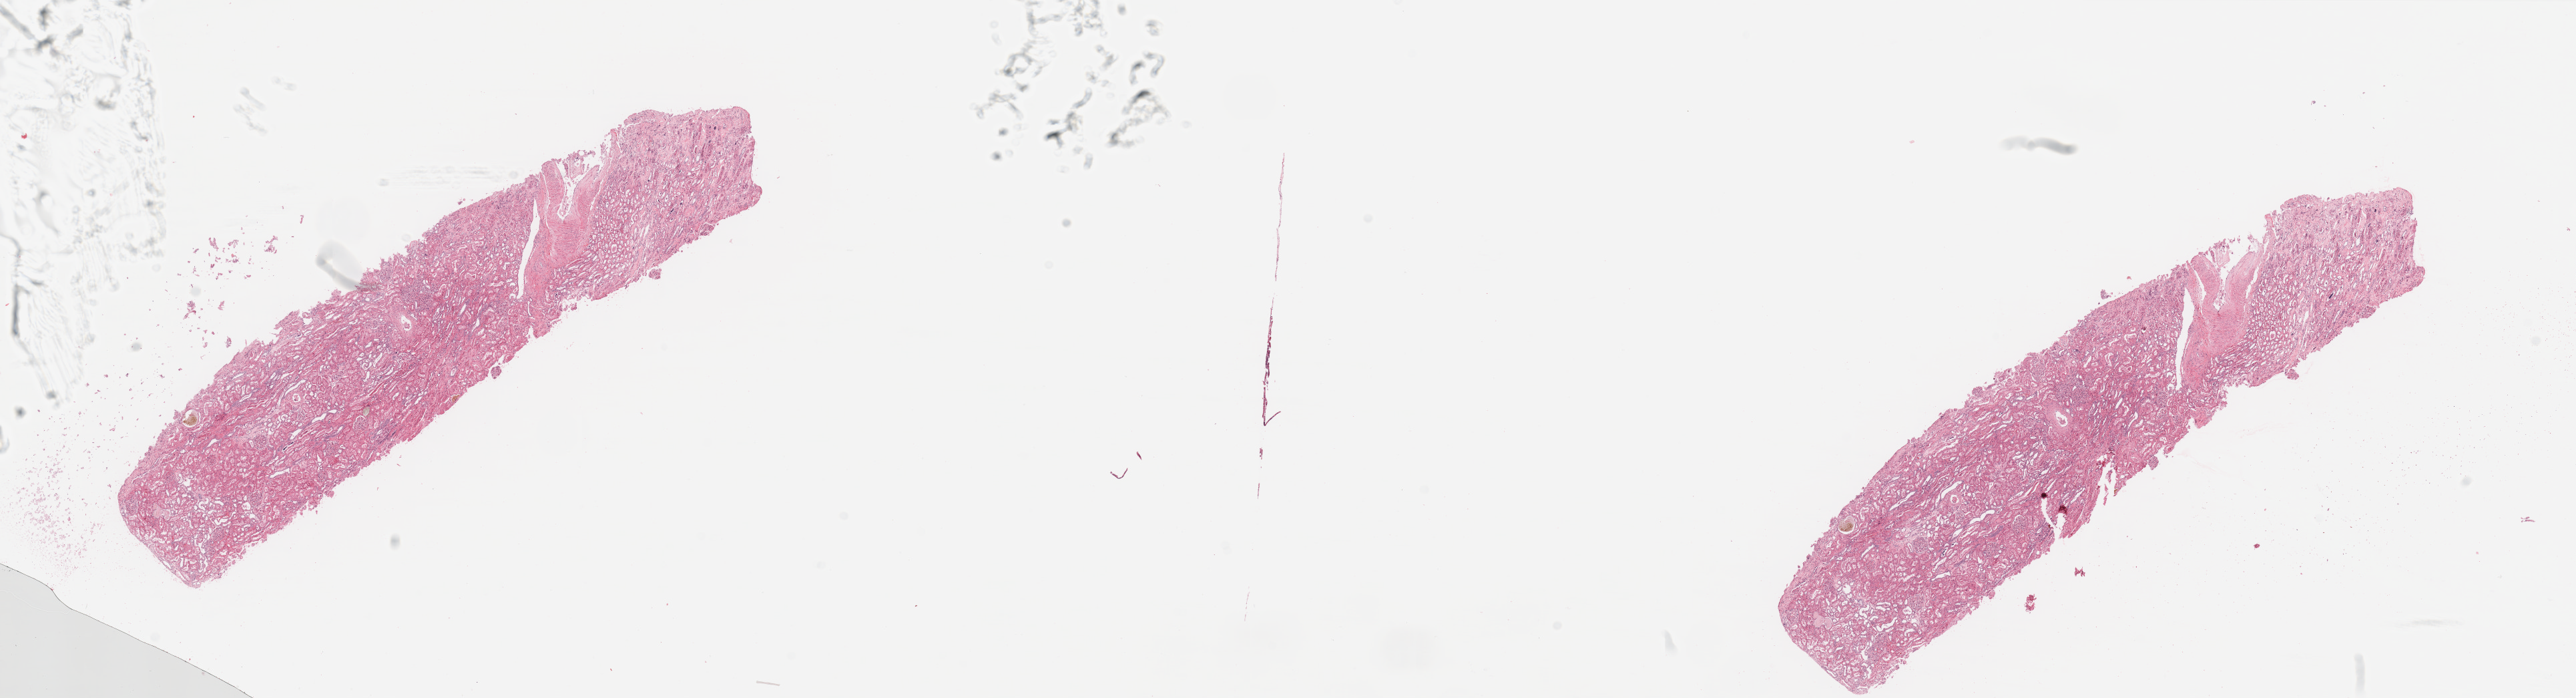
Hematoxylin and eosin (H&E) stained whole-slide image, low-resolution overview of the scanned area, about 30.5 x 8.3 mm (slide scanned at 20x). Normal (non-tumour) tissue sample, sampled site: kidney. Patient: male, age 74 years.
This section: normal (non-tumour) tissue from the same patient. Patient diagnosis: Renal cell carcinoma, NOS.